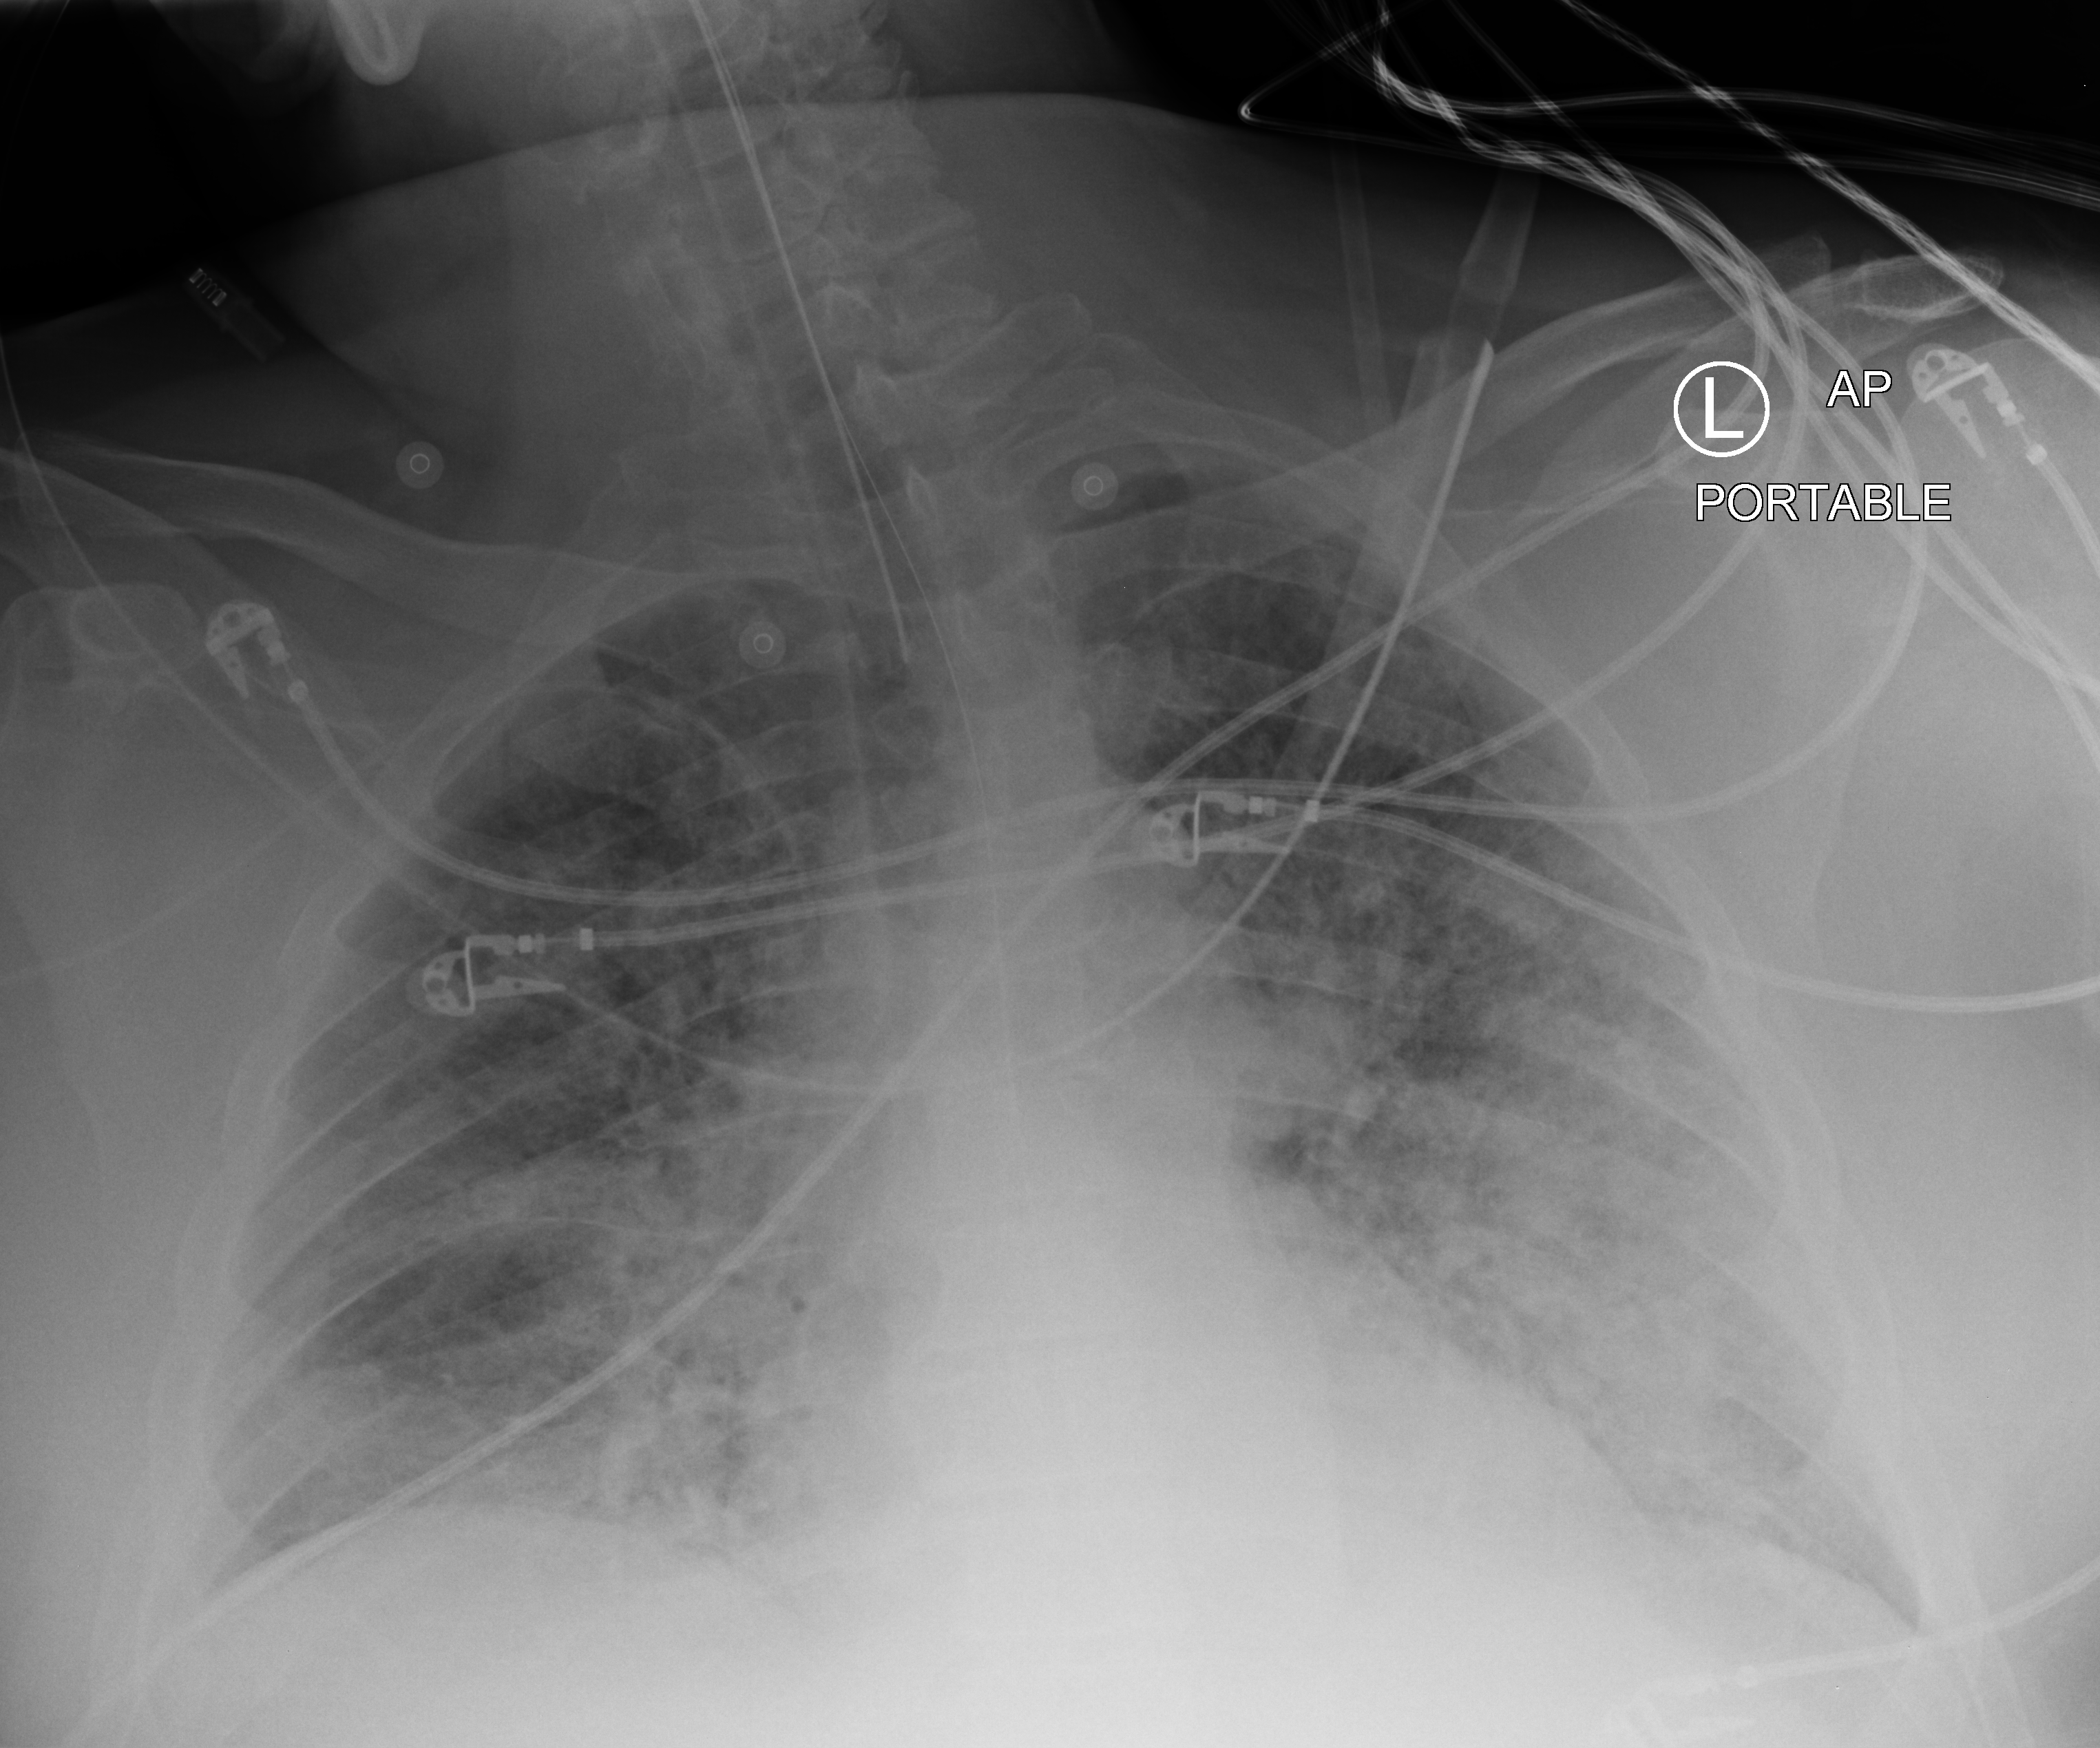
Portable chest radiograph; anteroposterior (AP) projection. Male patient hospitalised with COVID-19, age 60–74 years.
From the hospital-stay record, not from the radiograph (when in the stay this image was taken is not recorded):
- mechanically ventilated during this hospital stay: yes